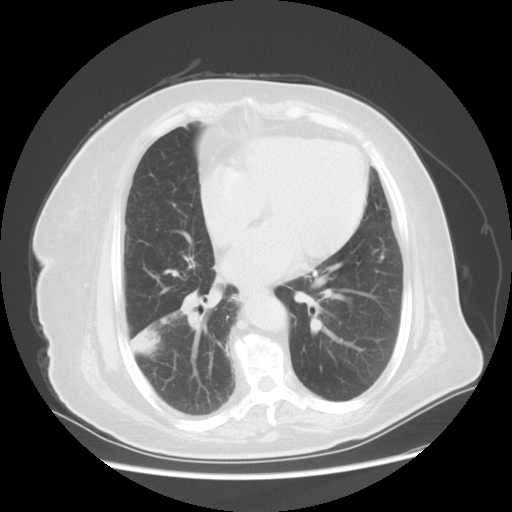
Chest CT, one axial slice. Position 24 of 56 along the scan axis. Reconstruction kernel STANDARD. Lung window (W 1500 / L -600 HU). 5 mm slice thickness. 512 × 512 image matrix, field of view 378 × 378 mm. Patient: female, 73 years. Case-level facts recorded for this patient, not image findings: clinical TNM (as recorded): T3 N0 M0.
Structures marked on this image (rectangle marked by the reading radiologist):
- lung tumour (recorded histology: adenocarcinoma): bounding box (x1, y1, x2, y2) in pixels: (125, 322, 165, 362)